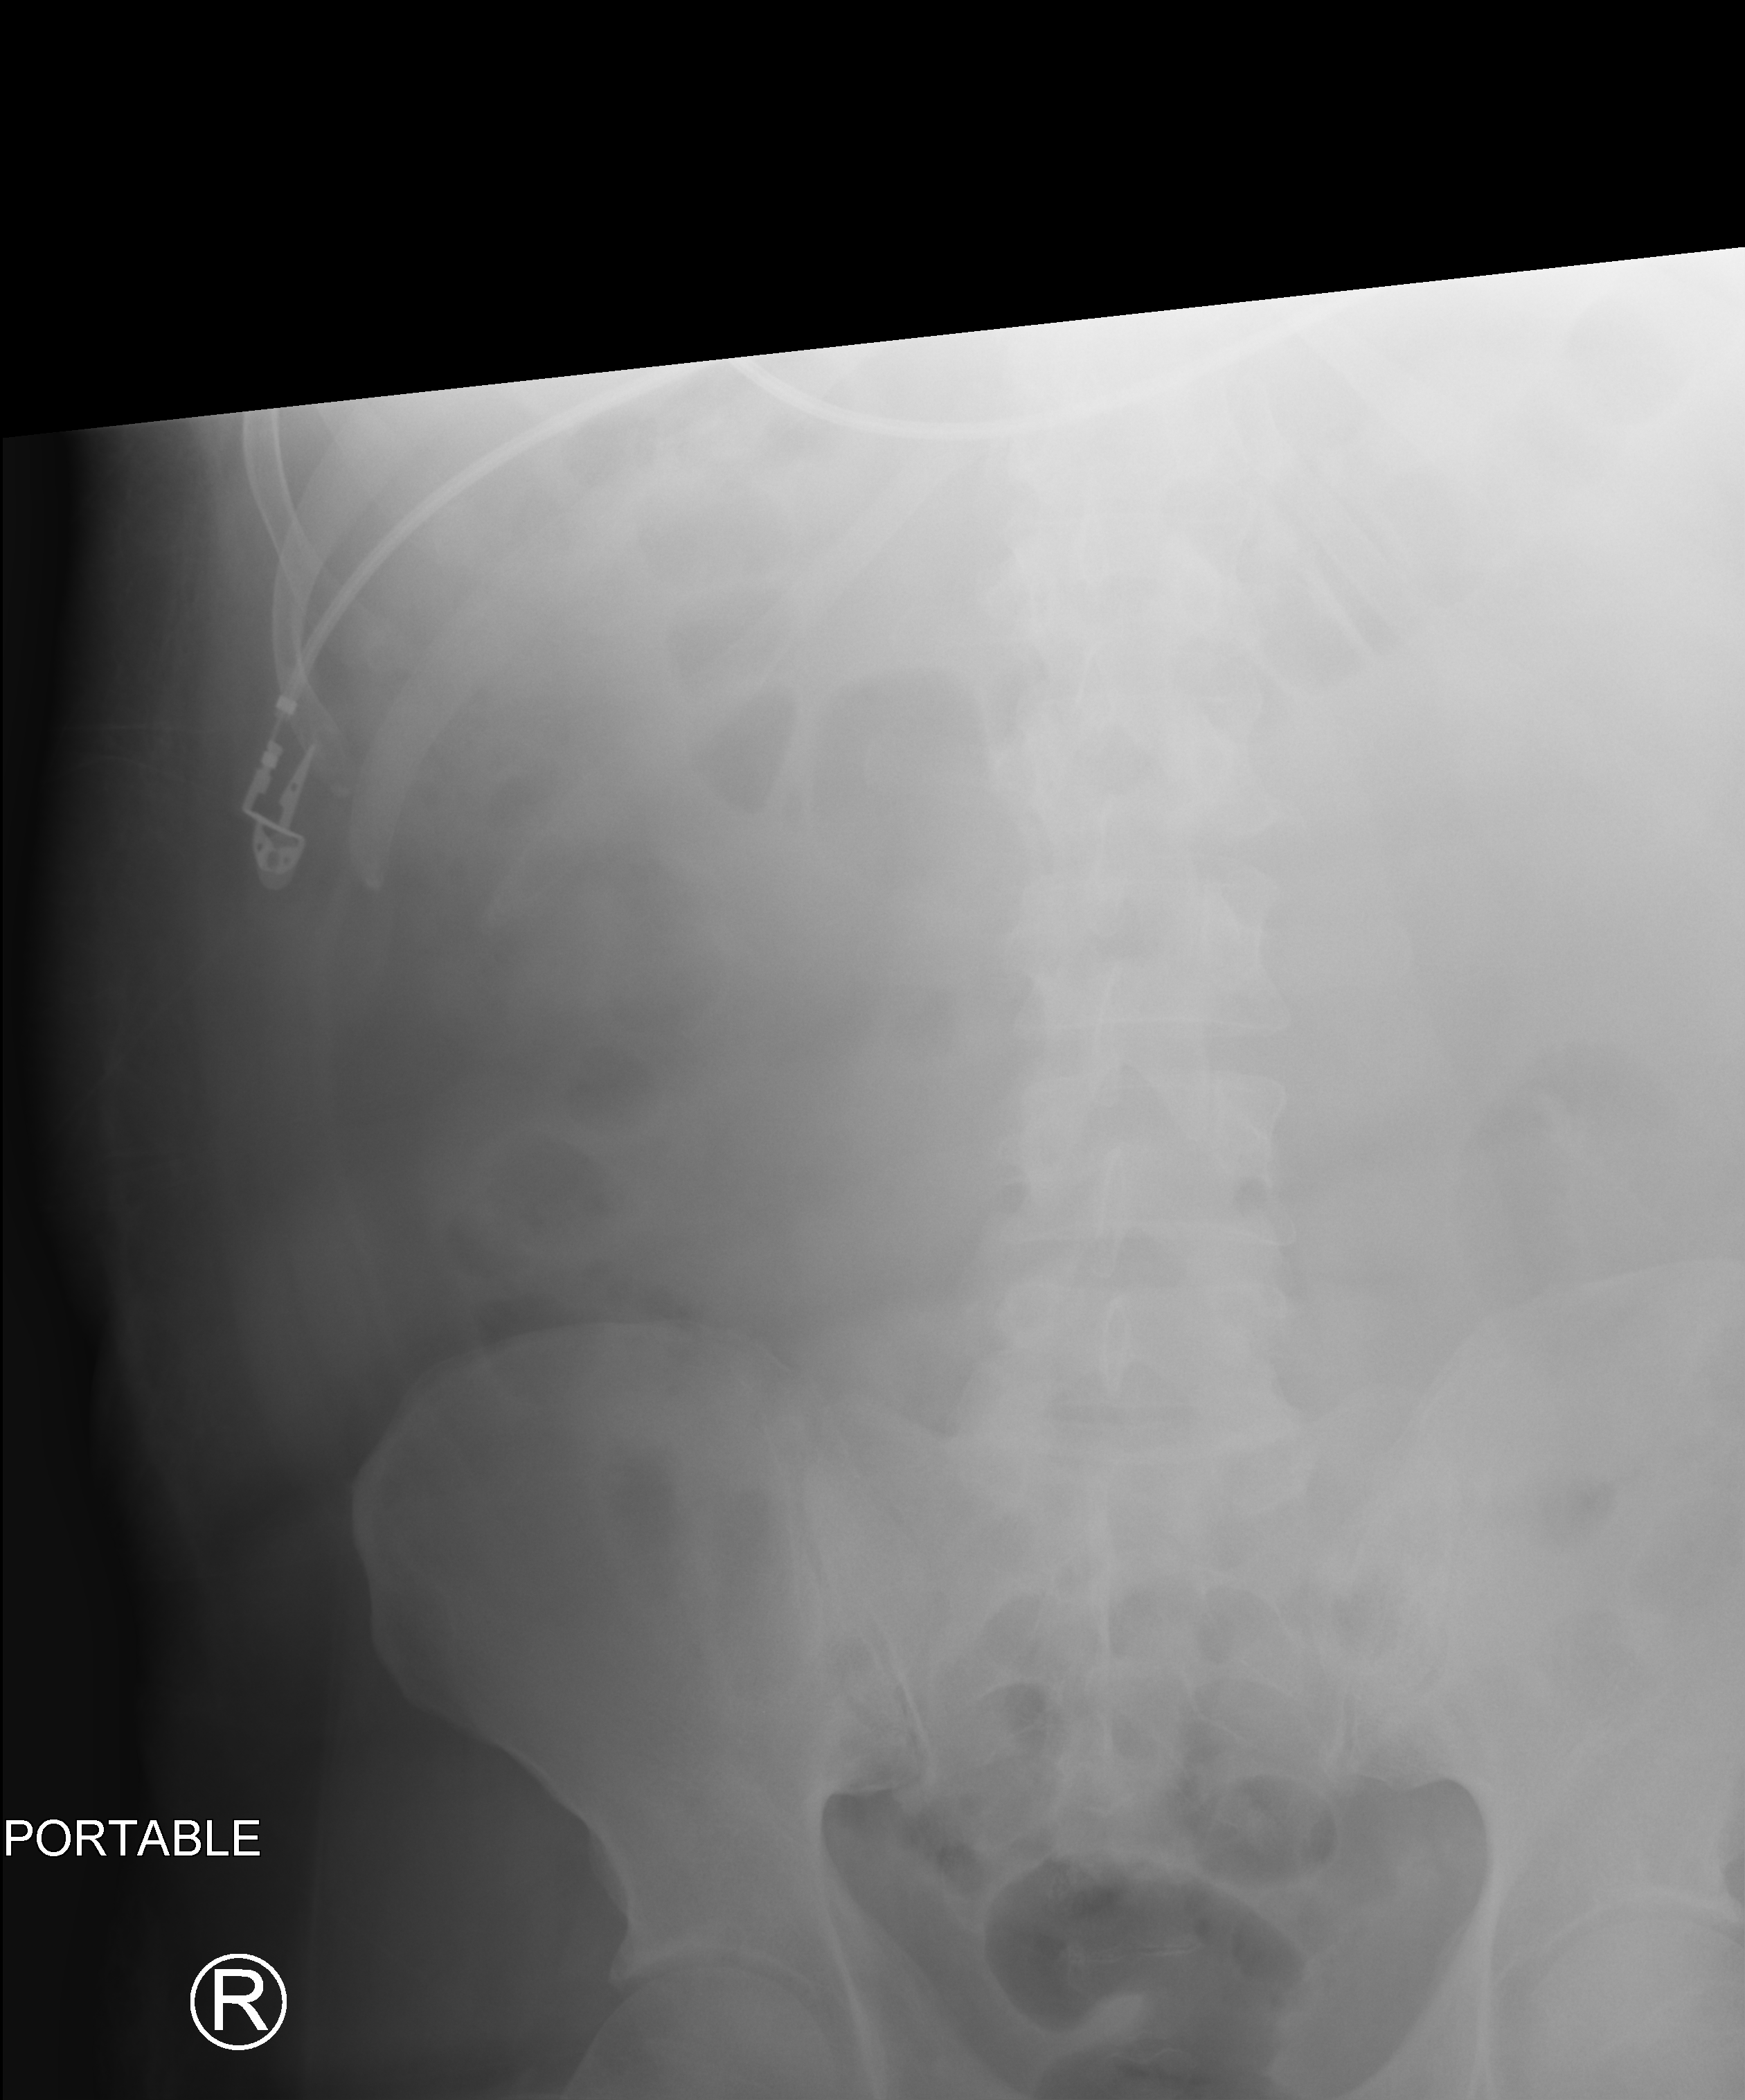
Portable abdomen radiograph, anteroposterior (AP) projection. Male patient hospitalised with COVID-19, age 18–59 years.
Hospital-stay facts (about this admission, not read from this image; timing relative to this image not recorded): smoking status (admission record): former; admitted to intensive care during this hospital stay: yes.